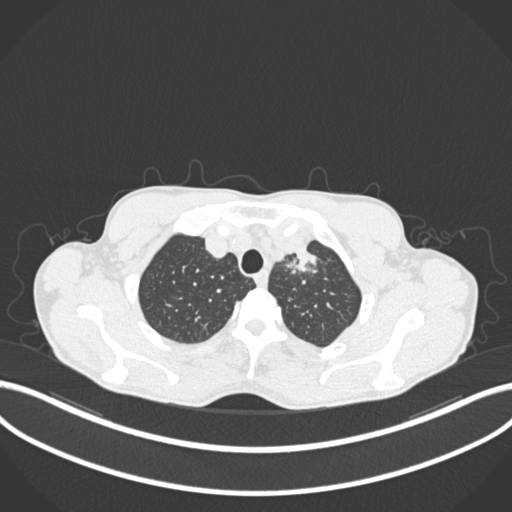
Chest CT, one axial slice; slice 177 of 211 in the series (ordered by position); reconstruction kernel B30f; 120 kVp; lung window (W 1500 / L -600 HU); 512 × 512 image matrix, field of view 400 × 400 mm. Male patient, age 58 years. From the clinical record (not read from this slice): clinical TNM (as recorded): T1c N1 M0.
Structures marked on this image (bounding box drawn by a radiologist):
- lung tumour (recorded histology: adenocarcinoma): bounding box [x1, y1, x2, y2] px = [281, 242, 323, 283]